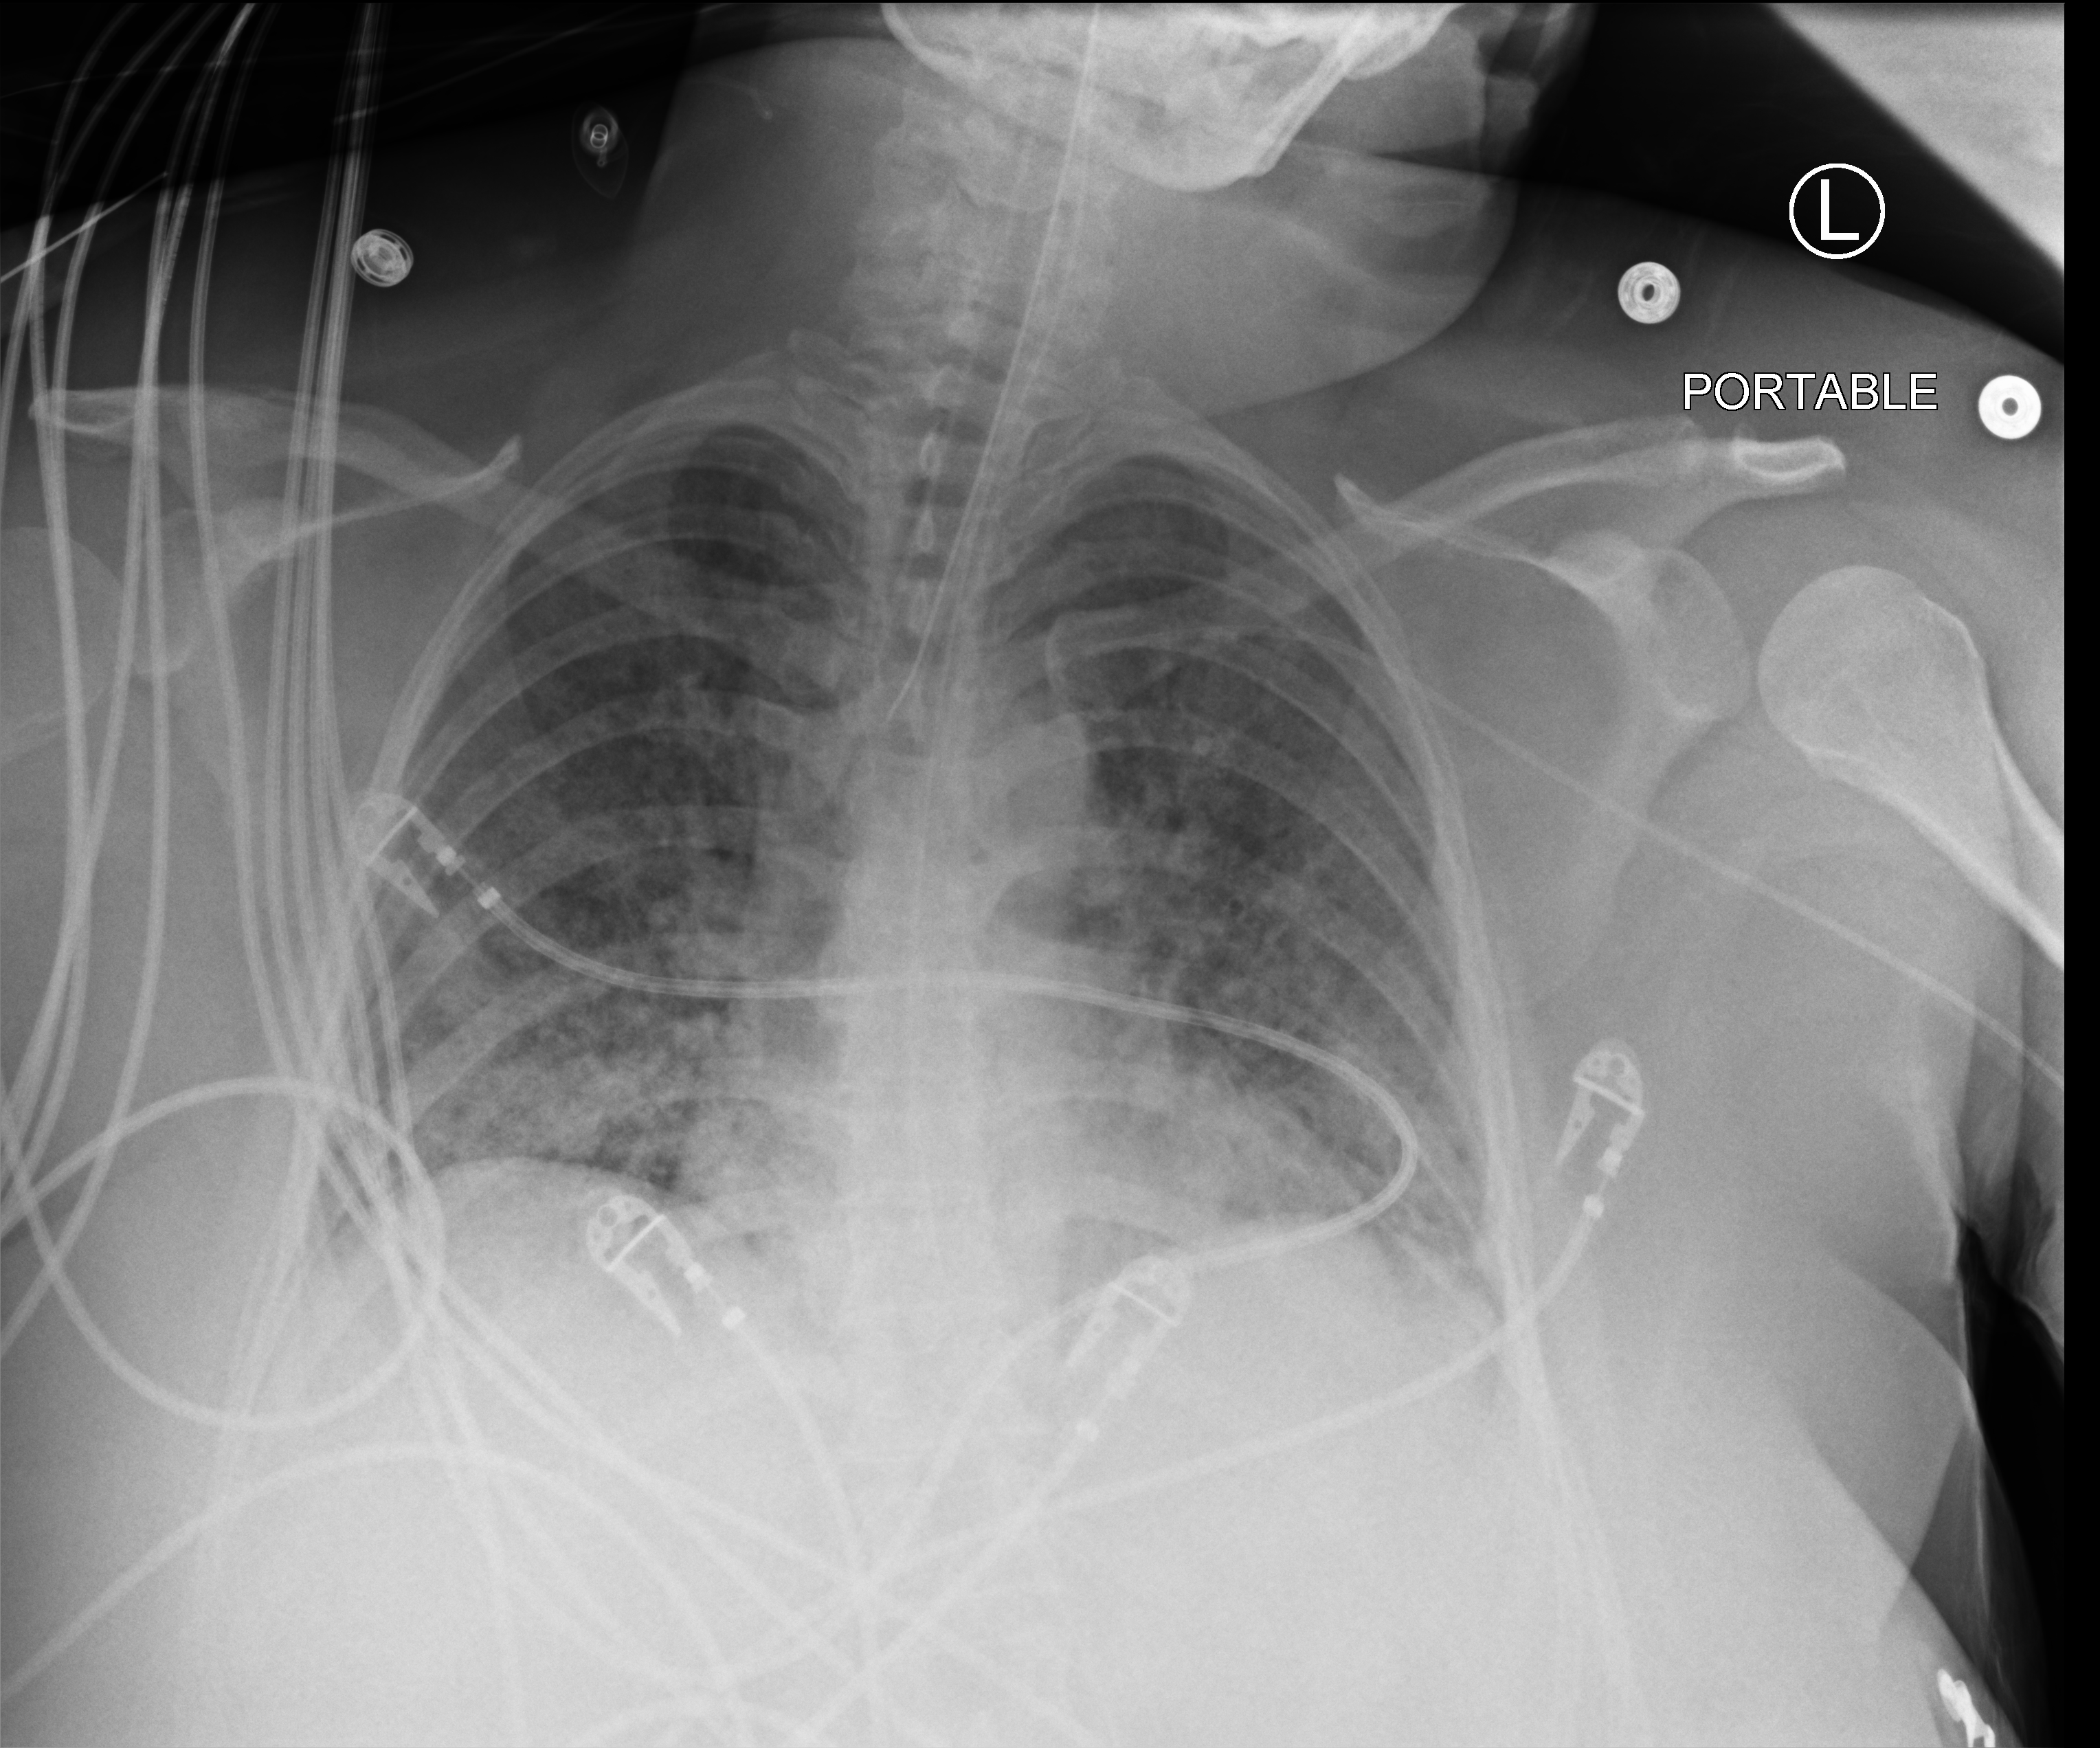
Chest X-ray (portable); anteroposterior (AP) projection. Female patient hospitalised with COVID-19, age 18–59 years.
From the hospital-stay record, not from the radiograph (when in the stay this image was taken is not recorded): mechanically ventilated during this hospital stay: yes.